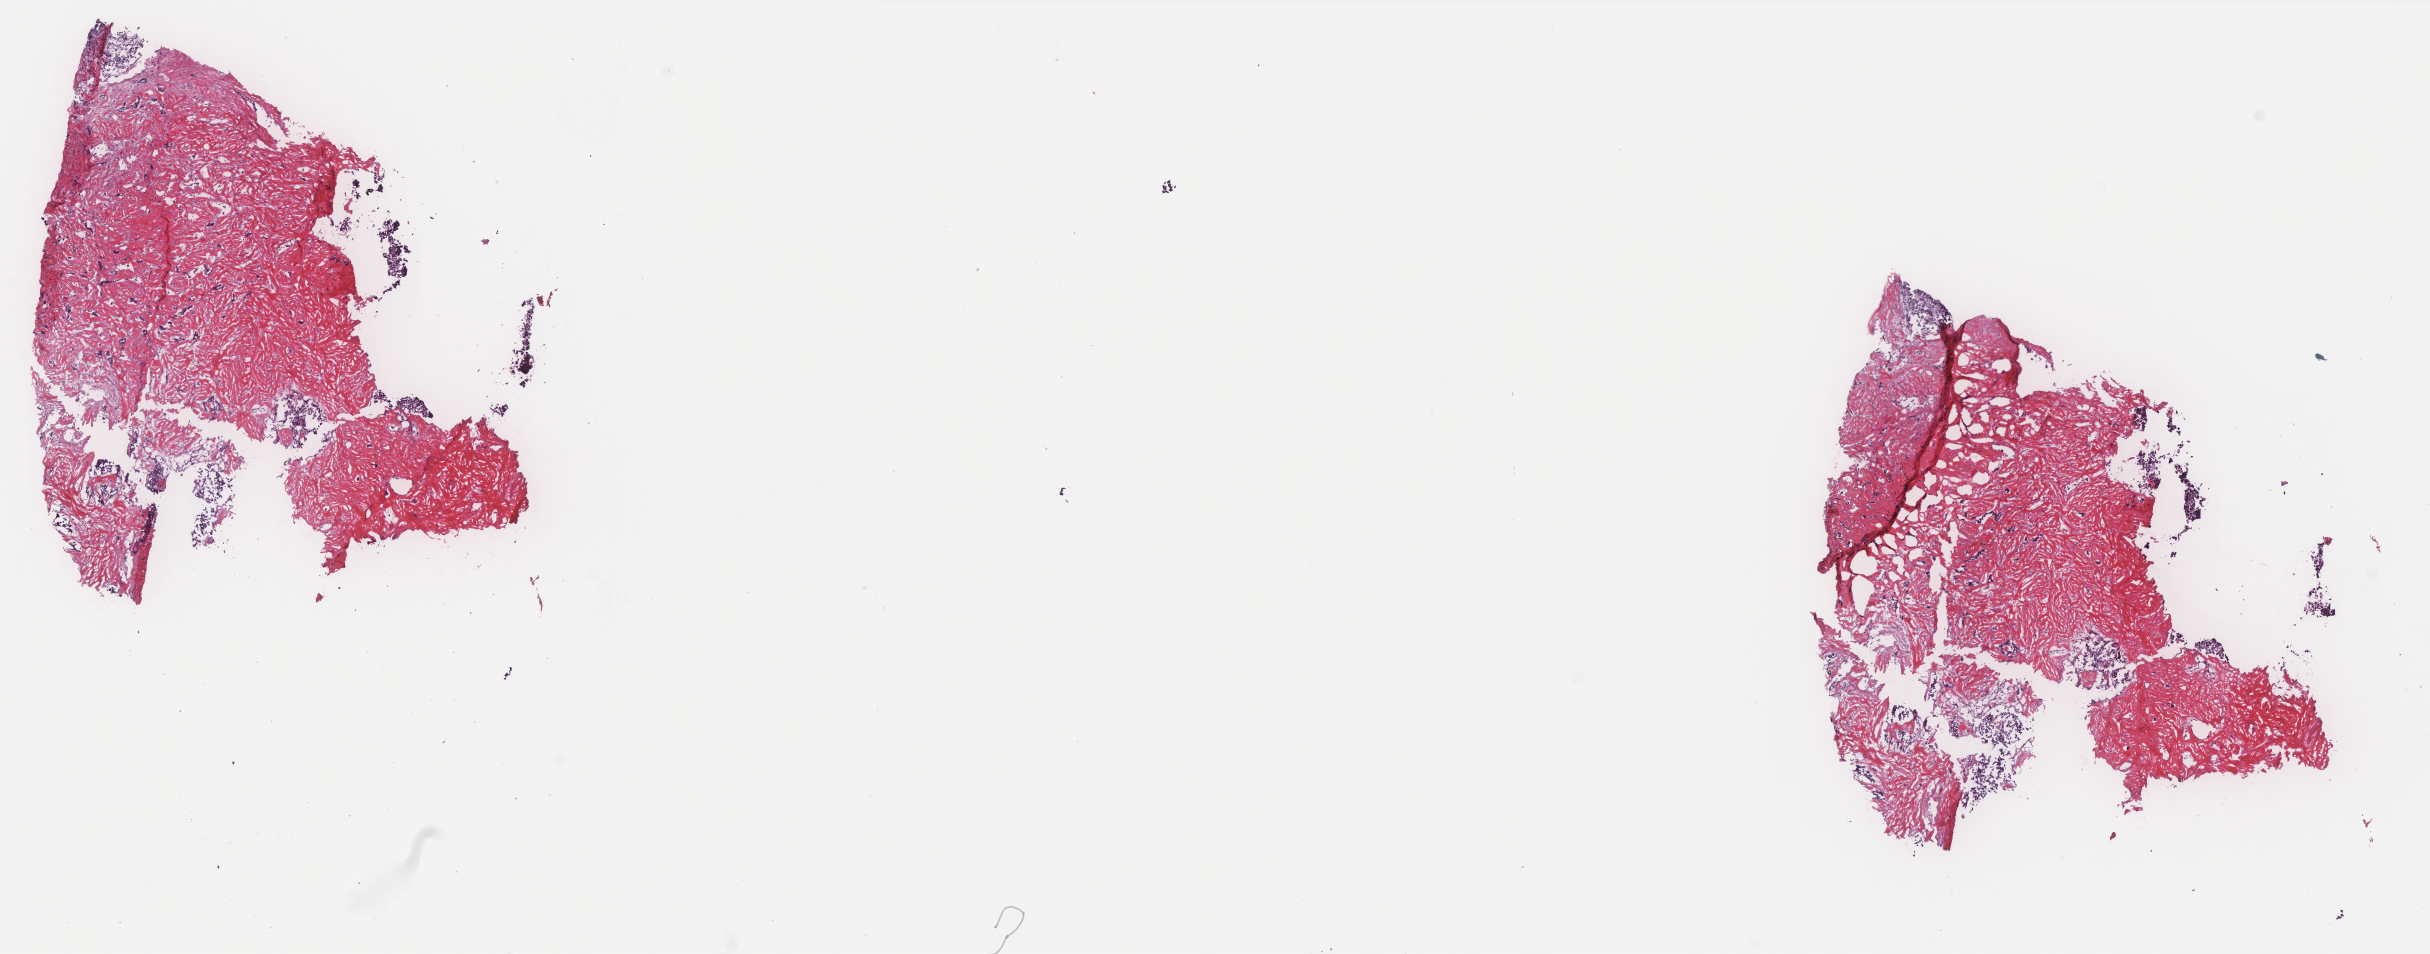
Digitized Hematoxylin and eosin (H&E) stained tissue section (whole slide) — low-resolution overview of the scanned area, about 19.5 x 7.6 mm (acquisition: 40x scan); frozen section from the bottom of the tissue portion; sample: primary tumour, breast. Female patient; age at initial diagnosis 69 years. Pathologist review of this section (percent, as recorded): tumour cells 70%, tumour nuclei 90%, normal cells 0%, stromal cells 30%, necrosis 0%. Infiltration values recorded for this section: lymphocyte infiltration 0%, monocyte infiltration 0%, neutrophil infiltration 0%.
* histologic diagnosis: Infiltrating duct carcinoma, NOS
* AJCC pathologic stage: IIIA (7th edition)
* lymph nodes positive (case pathology): 1 of 19 examined
* TNM: T2 N2 M0